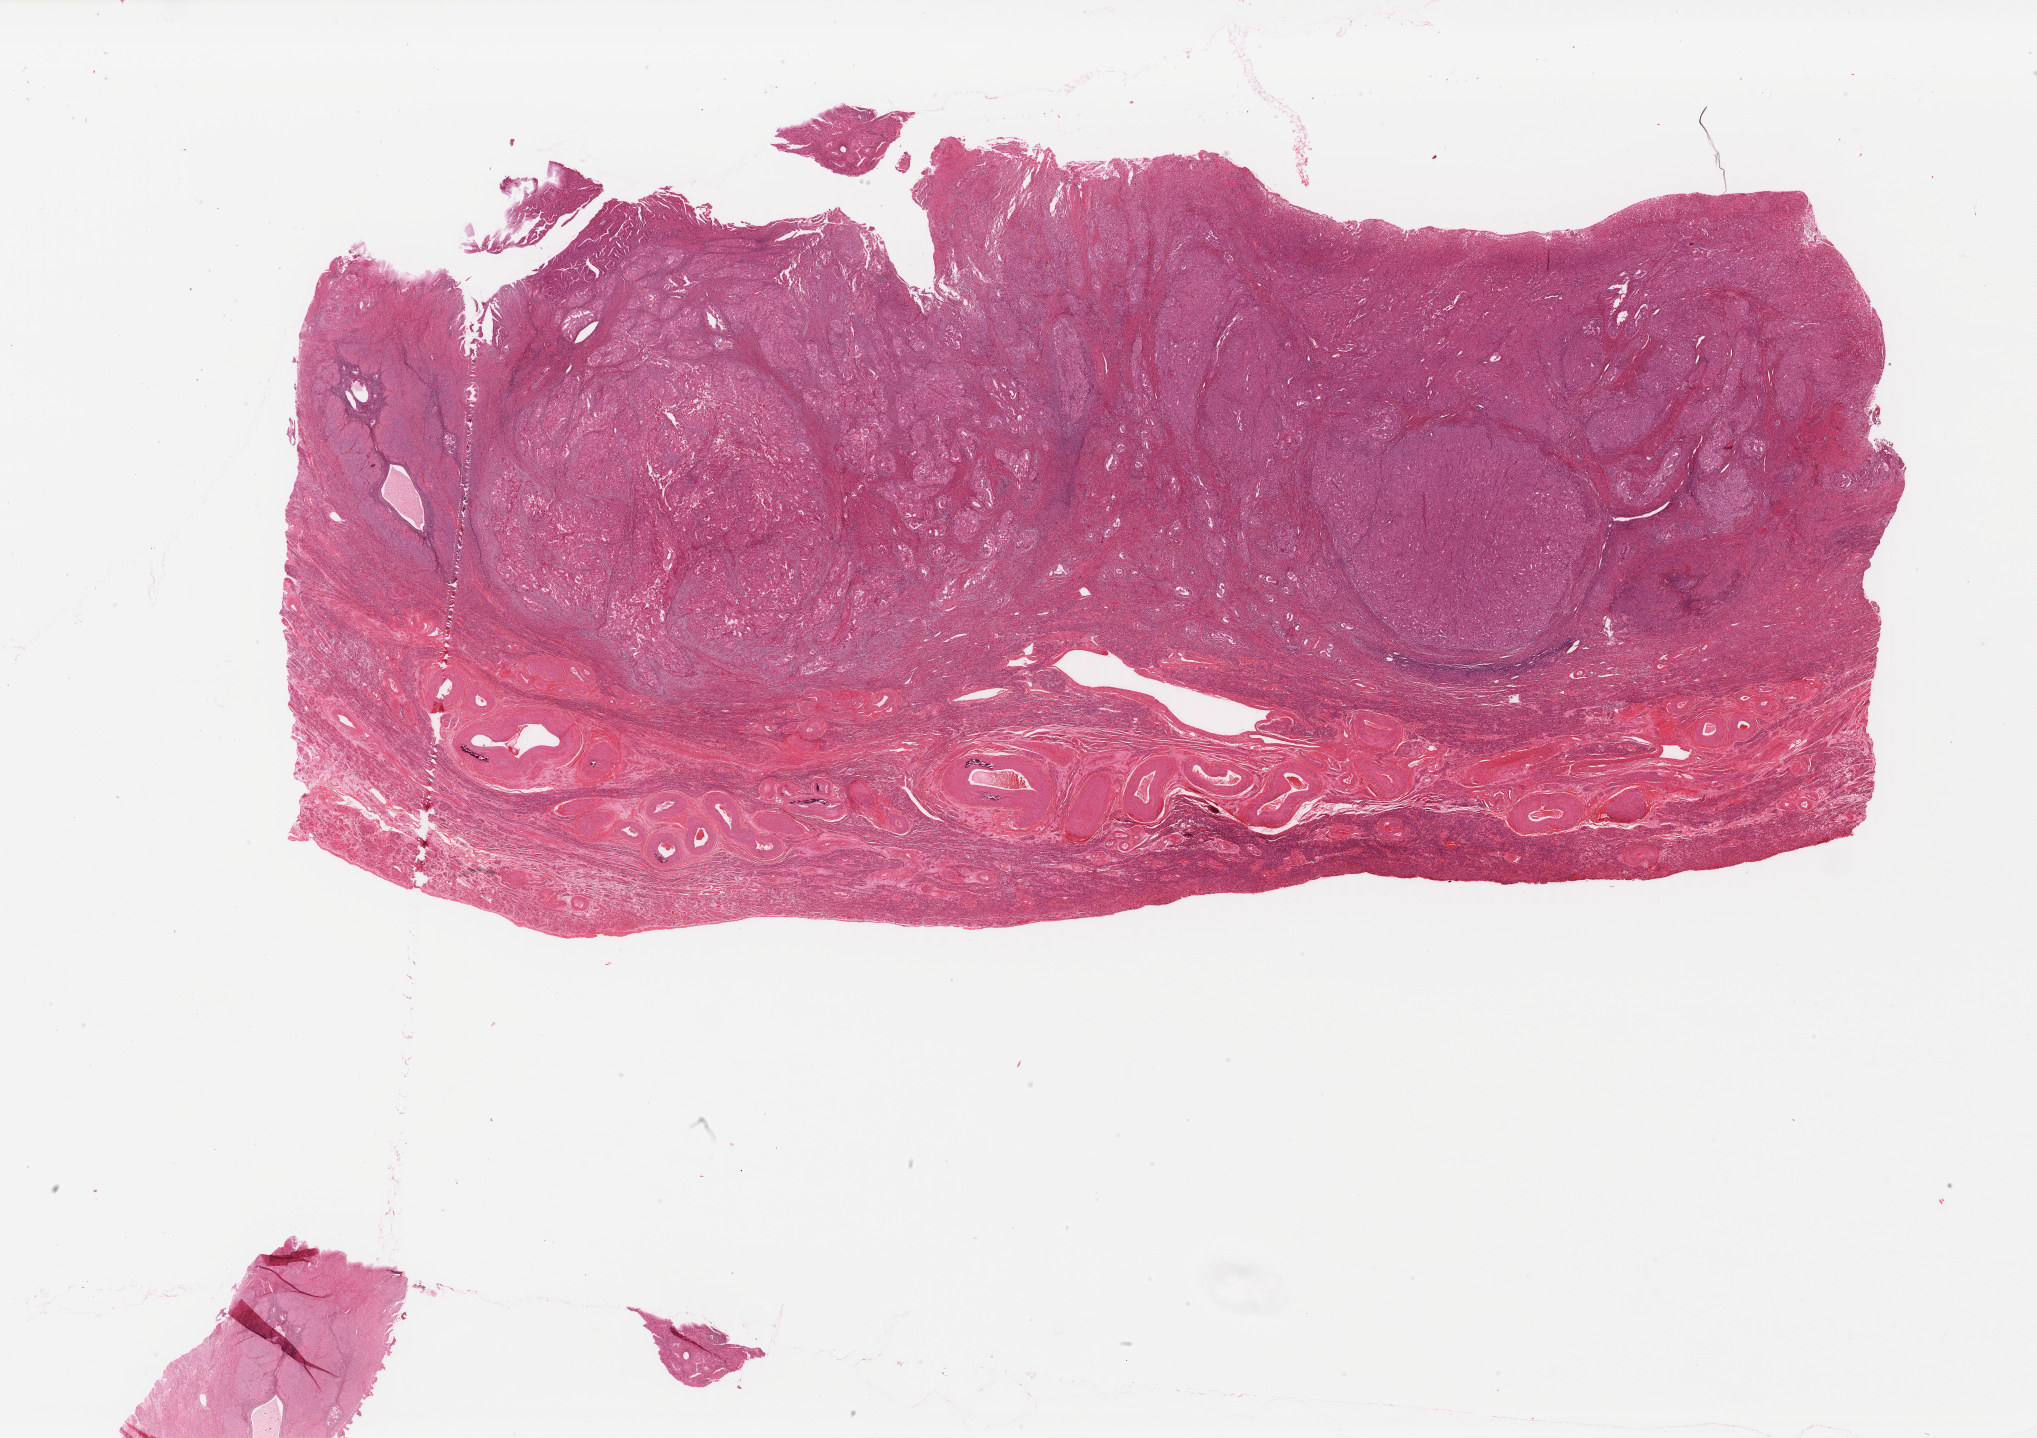
Whole-slide histology image, Hematoxylin and eosin (H&E) stained — shown as a low-resolution overview of the whole scanned area (about 32.2 x 22.7 mm, acquisition: 40x scan); FFPE section; primary tumour sample from the uterus. Female, age 72 years at initial diagnosis. Histologic grade: G3 (poorly differentiated).
FIGO stage: IIA. Histologic diagnosis: Endometrioid adenocarcinoma, NOS (endometrium).